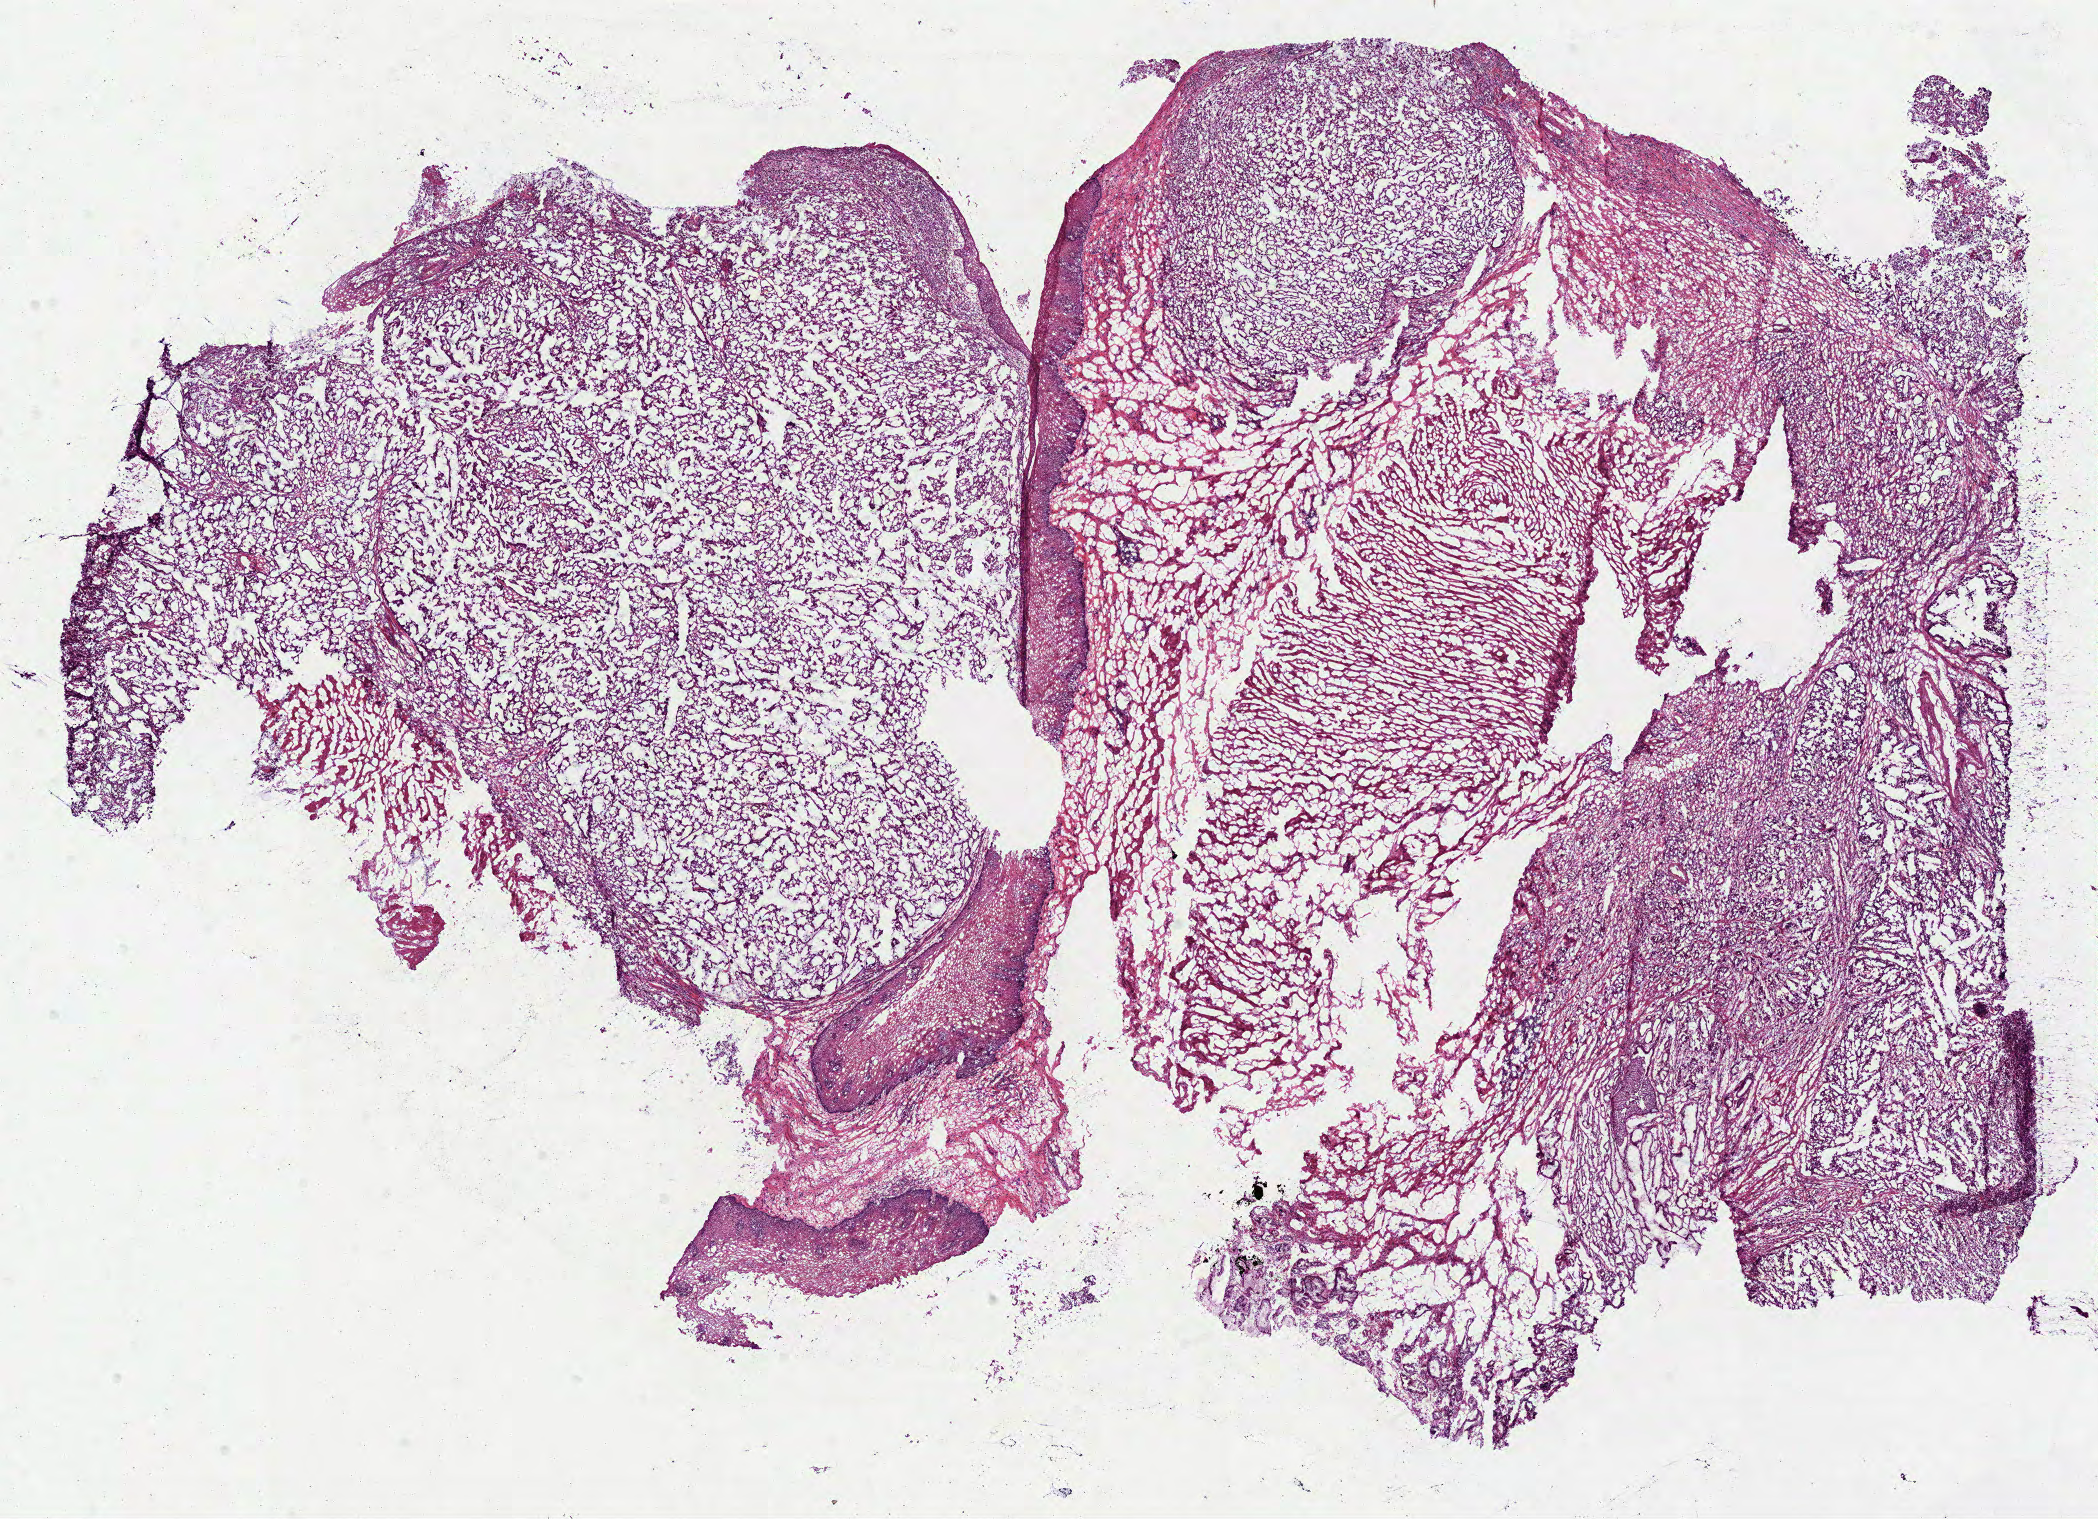
H&E whole-slide image — low-resolution overview of the scanned area, about 16.9 x 12.3 mm (slide scanned at 40x), frozen section from the bottom of the tissue portion, stomach, primary tumour sample. Male patient; age at initial diagnosis 80 years. Histologic grade: G2 (moderately differentiated). Composition of this section per pathologist review: tumour cells 70%, tumour nuclei 75%, normal cells 15%, stromal cells 15%, necrosis 0%.
Diagnosis: Adenocarcinoma, NOS (cardia, NOS). AJCC pathologic stage: IIB. Lymph nodes positive (case pathology): 2 of 6 examined.